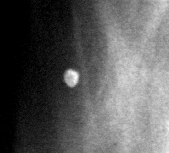
Crop from a digitized film mammogram around one marked abnormality, right breast, MLO view.
Finding: calcifications, morphology coarse; BI-RADS assessment category 2; subtlety rating 4 on a 1 (subtle) to 5 (obvious) scale; benign without callback (not worked up further).